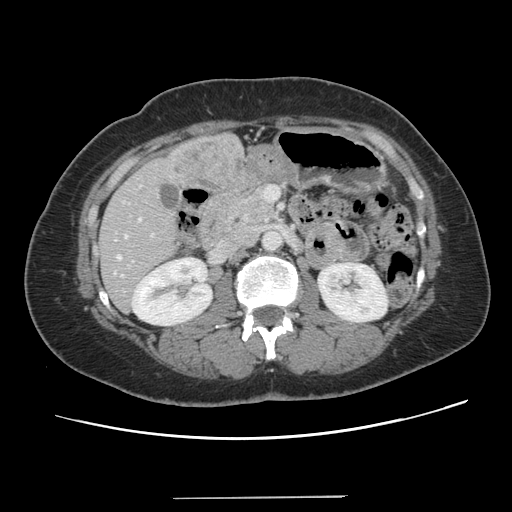
Contrast-enhanced abdominal CT, one axial slice; slice 53 of 141 in the series (ordered by position); intravenous contrast given; soft-tissue window (W 400 / L 40 HU); 2.5 mm slice thickness; 512 × 512 image matrix. Female patient, age 53 years. From the clinical record (not read from this slice): diagnosis: colorectal cancer liver metastases, imaged before liver resection; multiple liver metastases: no; largest metastasis: 14.5 cm.
Annotated regions visible in this slice (outlined manually by an expert reader):
- hepatic veins: bounding box <116,235,126,260> (left, top, right, bottom; pixels)
- liver: <98,135,243,311>
- planned liver remnant (the part of the liver to remain after resection): <97,218,178,311>
- portal vein (with intrahepatic branches): <139,219,153,236>
- liver metastasis: <172,139,242,189>